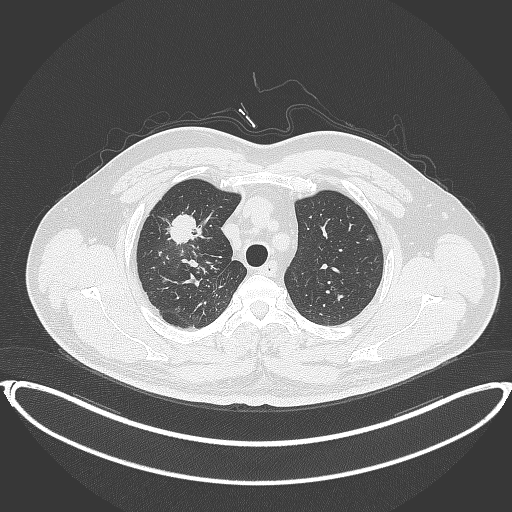
Chest CT, one axial slice; position 309 of 399 along the scan axis; 120 kVp; lung window (W 1500 / L -600 HU); 1 mm slice thickness; 512 × 512 image matrix. Patient: male, 53 years. From the clinical record (not read from this slice): clinical TNM (as recorded): T2a N0 M0.
Structures marked on this image (bounding box drawn by a radiologist):
- lung tumour (recorded histology: adenocarcinoma): bounding box (x1, y1, x2, y2) in pixels: (168, 210, 201, 250)